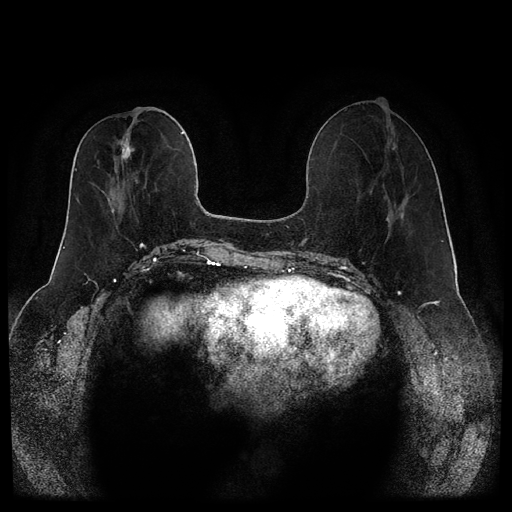
Breast MRI (dynamic contrast-enhanced, multi-phase), one axial slice; position 41 of 116 along the scan axis; dynamic contrast-enhanced series, time point 2 of 5 at this slice position (early post-contrast); 1.5 T; TE 2.6 ms, TR 5.3 ms; 2 mm slice thickness; 512 × 512 image matrix. Patient: female, 46 years.
Outlined on this slice (semi-automatically segmented with operator editing):
- breast lesion (labelled 'tumour' in the annotation; benign lesions carry a separate 'benign' label): bounding box [x1, y1, x2, y2] px = [114, 131, 135, 163]